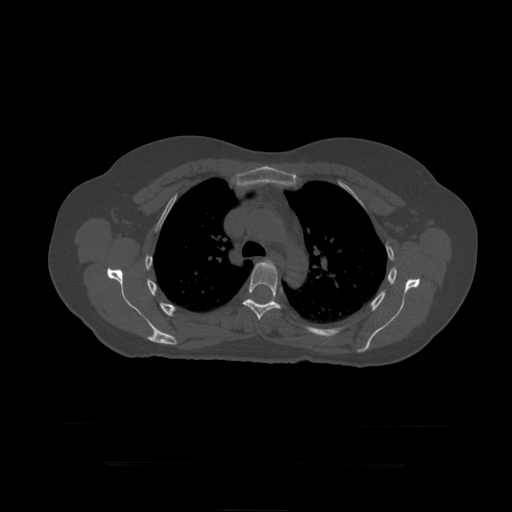
CT including the spine, one axial slice. Slice 320 of 399 in the series (ordered by position). Reconstruction kernel STANDARD. 120 kVp. Bone window (W 1800 / L 400 HU). 1.25 mm slice thickness. 512 × 512 image matrix, field of view 450 × 450 mm. Patient age 41 years. Case-level facts recorded for this patient, not image findings: primary cancer: breast.
Structures marked on this image (semi-automatic segmentation, software-assisted and operator-edited):
- T5 vertebra: bounding box <265,260,273,264> (left, top, right, bottom; pixels)
- T6 vertebra: <242,260,281,320>
- T7 vertebra: <270,299,275,303>